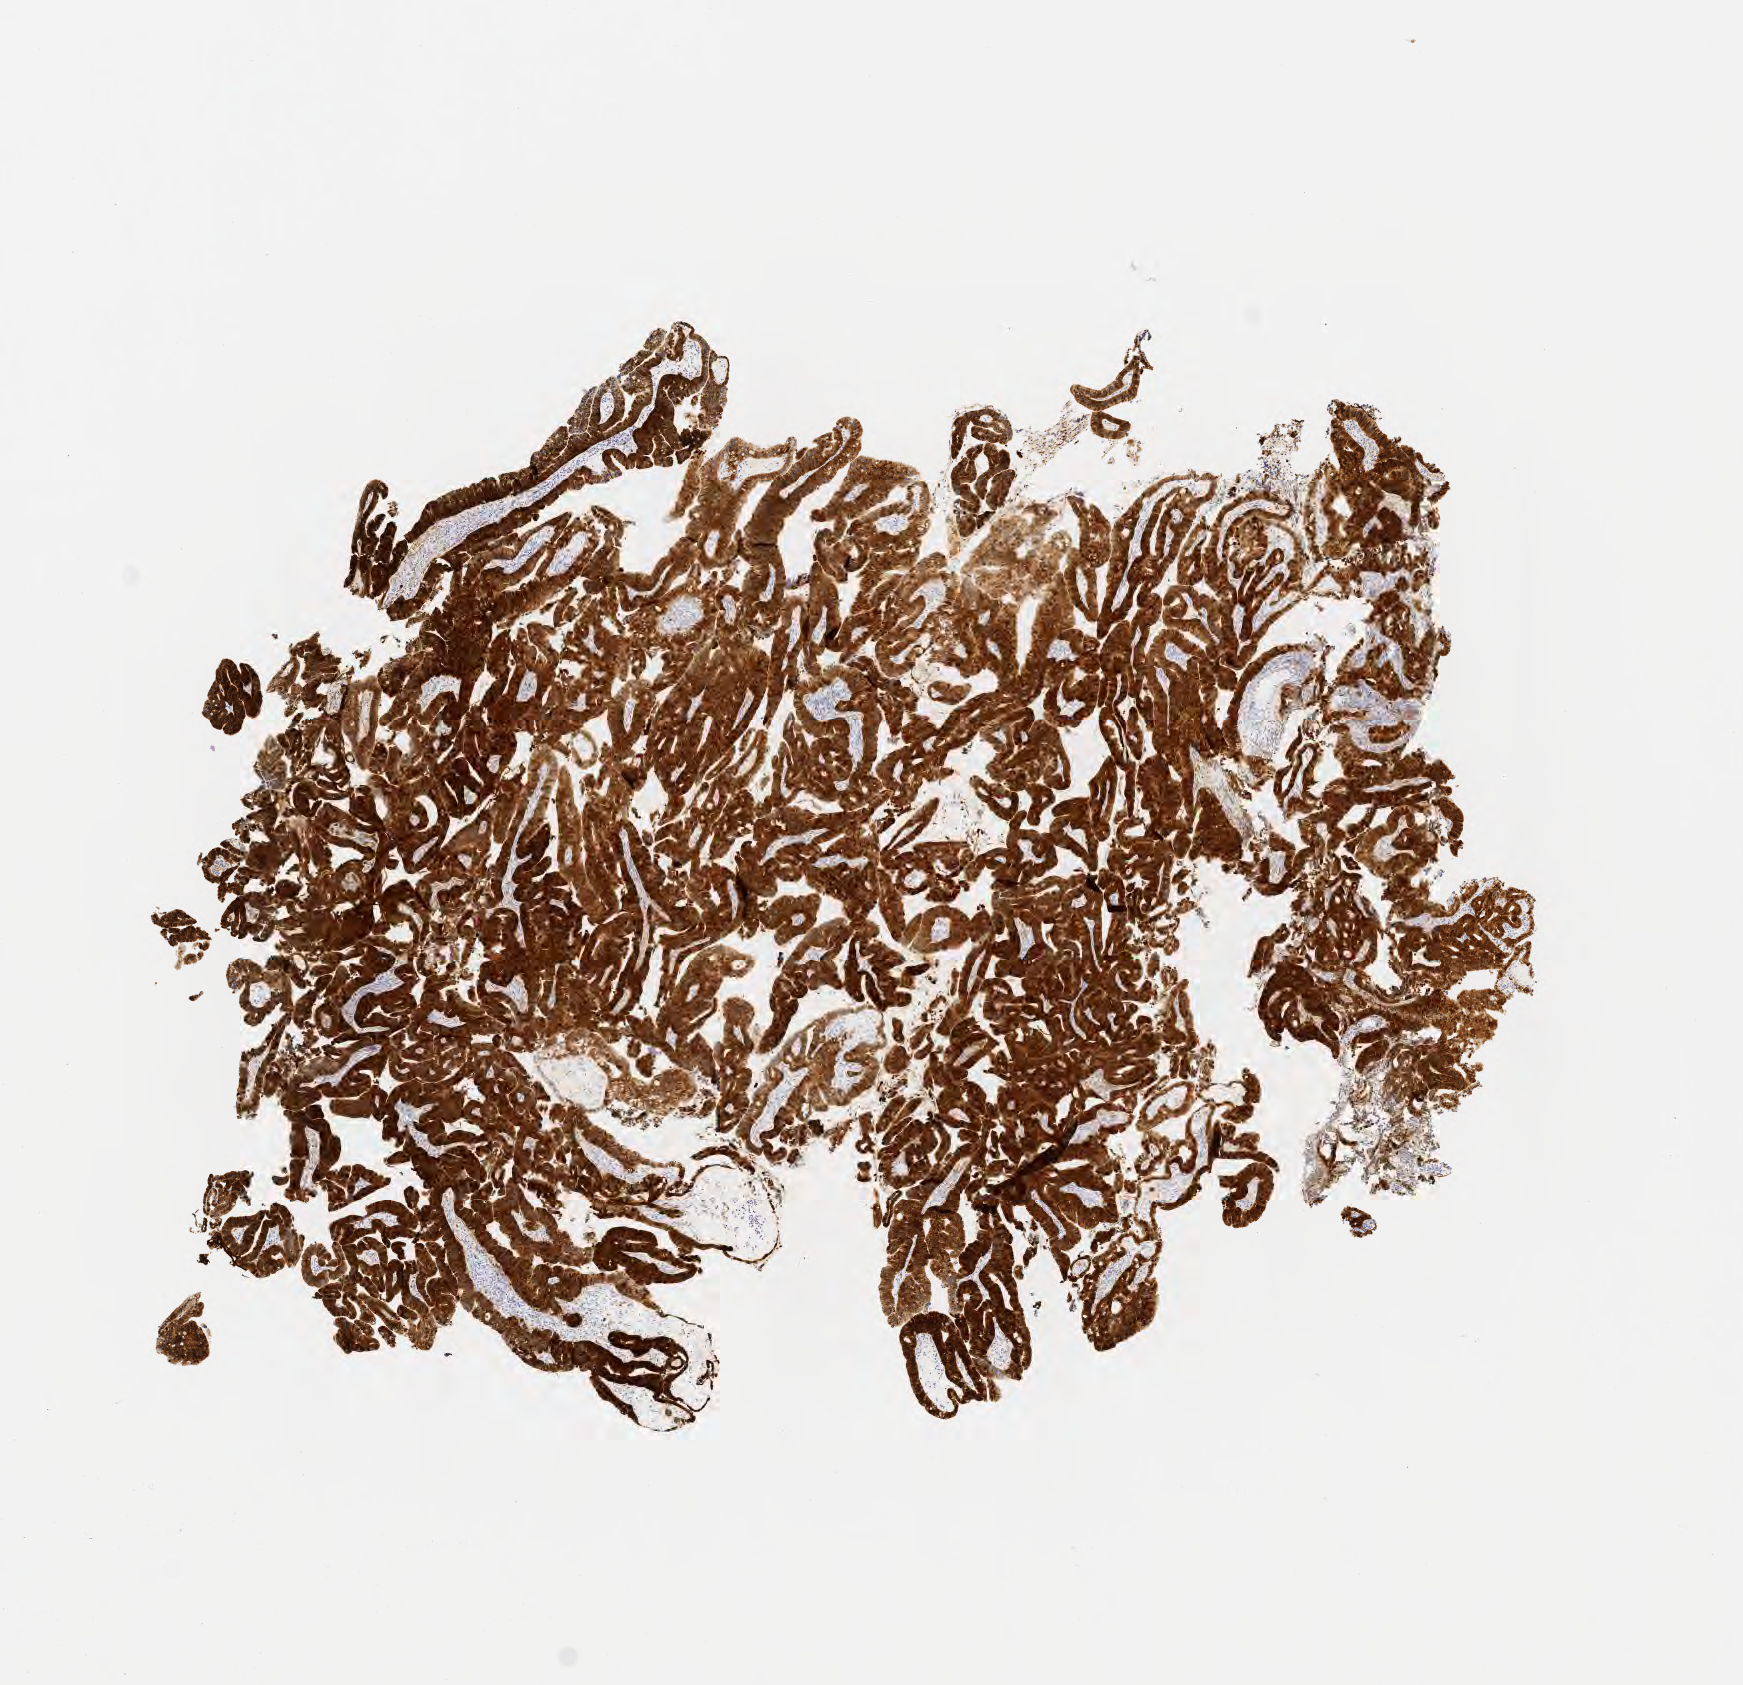
Immunohistochemistry (IHC) whole-slide image stained for p16 (p16INK4a), low-resolution overview of the scanned area, about 7.0 x 6.8 mm; tumor tissue; site: cervix. Female patient, 45 years old.
Histologic diagnosis: Adenocarcinoma, NOS.